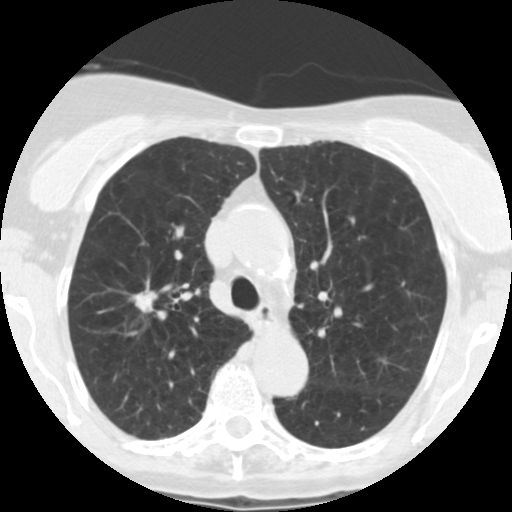
Low-dose screening chest CT, axial slice, first (baseline) screen, lung window (W 1500 / L -600 HU), 2.5 mm slice thickness, standard (soft-tissue) reconstruction kernel (STANDARD), slice 174 of 246 in the series, 512 × 512 image matrix. Female, age 67 years at enrolment. Former smoker at enrolment.
Expert-annotated lung lesion, bounding box (x1, y1, x2, y2) in pixels: (114, 280, 172, 322). The screening reader recorded 6 non-calcified nodules or masses ≥4 mm on this exam; which of them this box marks is not recorded. Later outcome: lung cancer diagnosed 15 days after this screen — adenocarcinoma, NOS, right upper lobe, moderately differentiated (G2), stage IA (AJCC 6th edition), 14 mm at pathology.